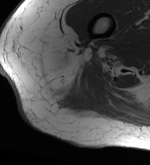
MRI of an extremity soft-tissue mass, one axial slice; position 11 of 56 along the scan axis; MR volume resampled by the dataset authors to the PET/CT grid (not the native acquisition matrix); 3.27 mm slice thickness; 150 × 165 image matrix. Female patient. From the clinical record (not read from this slice): histological type: epithelioid sarcoma with vascular differentiation; site of the primary tumour: right buttock.
Outlined on this slice (expert contour drawn on MRI and transferred to this co-registered scan by the dataset authors):
- gross tumour volume (mass): bounding box <64,65,70,68> (left, top, right, bottom; pixels)